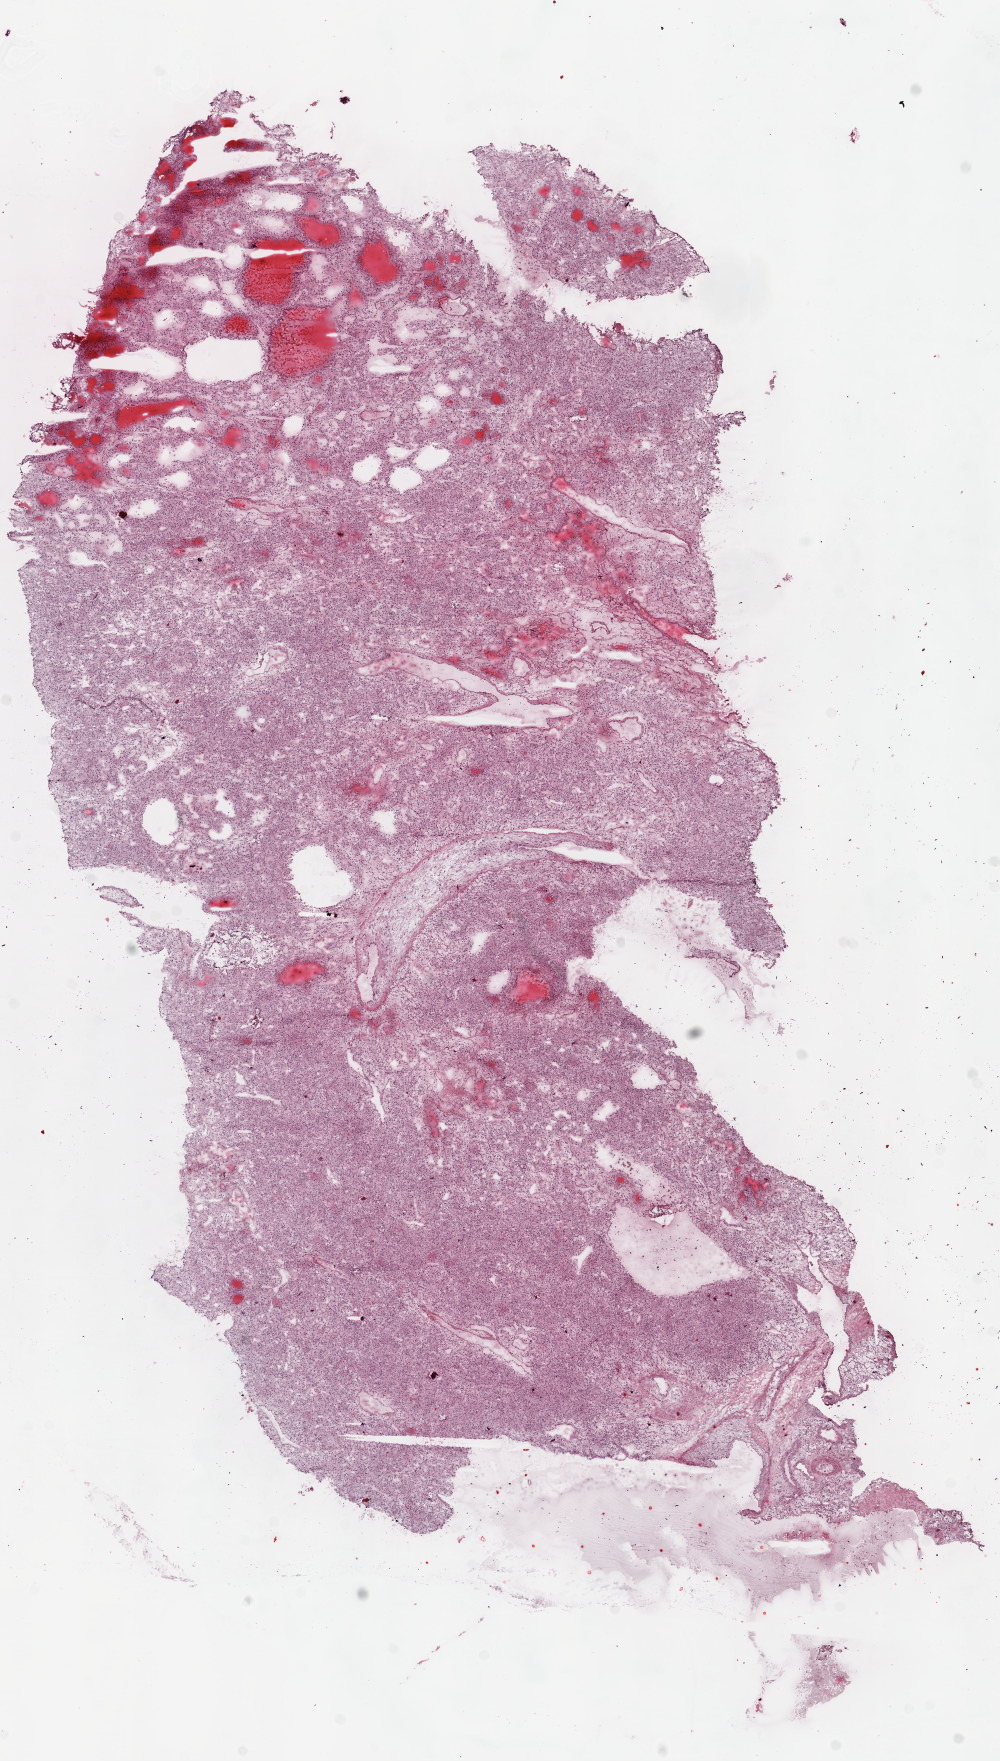
Whole-slide histology image, H&E — low-resolution overview of the scanned area, about 8.0 x 14.1 mm (slide scanned at 20x); frozen section from the top of the tissue portion; primary tumour sample from the kidney. Female, age 43 years at initial diagnosis. Histologic grade: G3 (poorly differentiated). Composition of this section per pathologist review: tumour cells 100%, tumour nuclei 97%, necrosis 0%. Inflammatory infiltration, as recorded: lymphocyte infiltration 1%.
AJCC pathologic stage: I. Pathologic diagnosis: Clear cell adenocarcinoma, NOS.